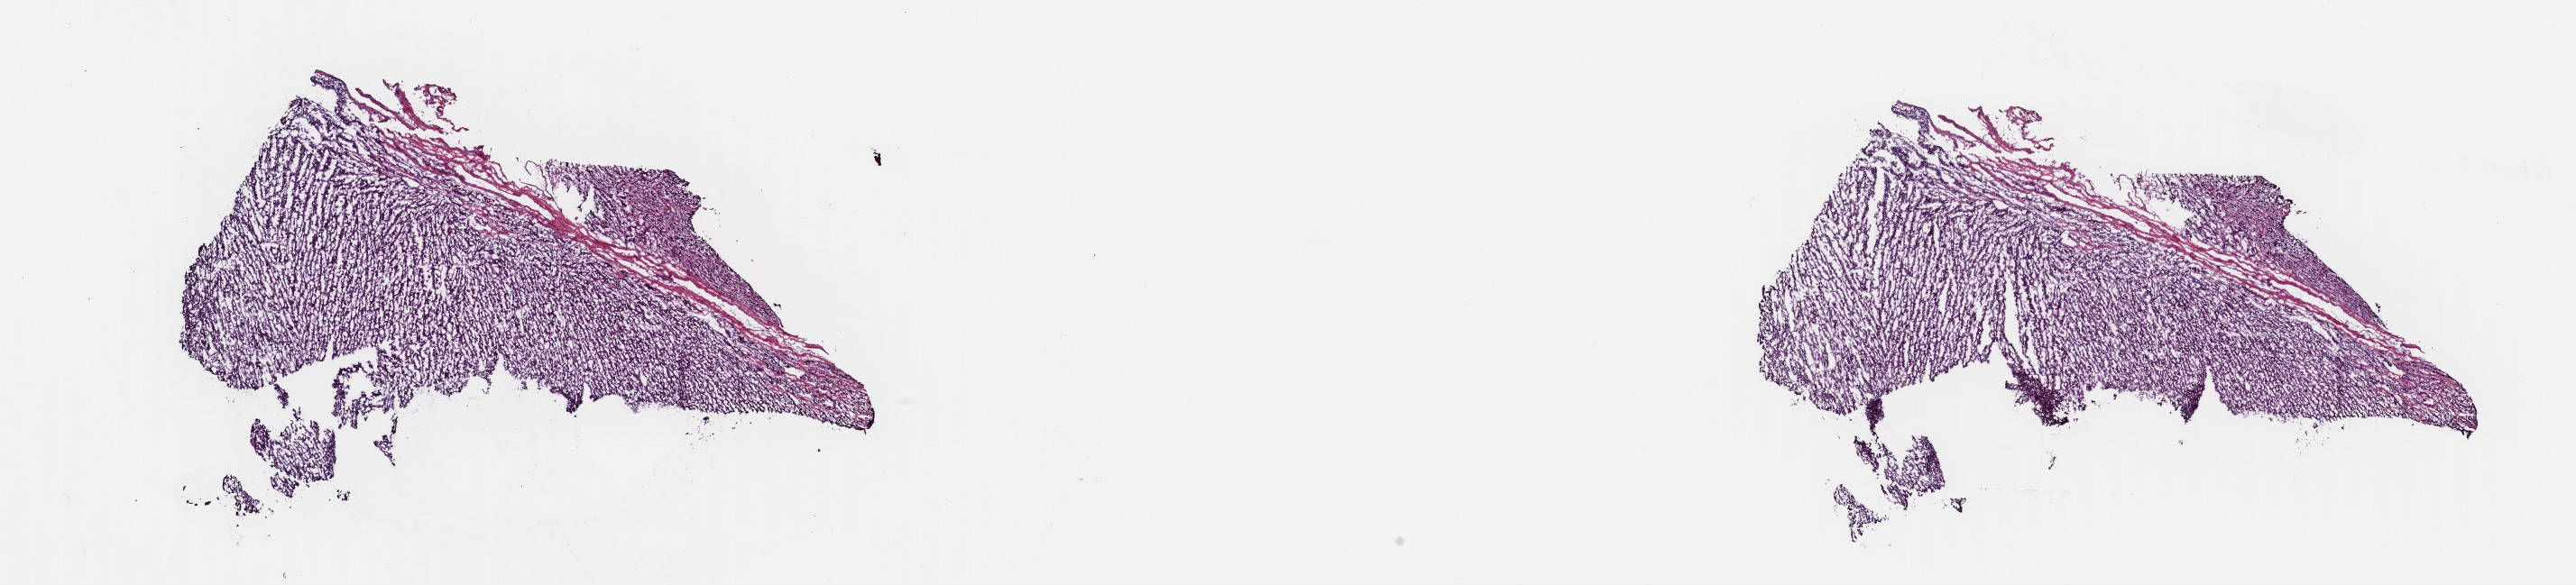
Hematoxylin and eosin (H&E) stained whole-slide image — shown as a low-resolution overview of the whole scanned area (about 22.6 x 5.1 mm, from a 40x scan); frozen section from the top of the tissue portion; primary tumour sample from the adrenal cortex. Patient: male, age at initial diagnosis 61 years. Pathologist review of this section (percent, as recorded): tumour cells 99%, tumour nuclei 99%, normal cells 0%, stromal cells 1%, necrosis 0%. Inflammatory infiltration, as recorded: lymphocyte infiltration 0%, monocyte infiltration 0%, neutrophil infiltration 0%.
Laterality: left. Lymph nodes positive (case pathology): 6 of 8 examined. Histologic diagnosis: Adrenal cortical carcinoma.